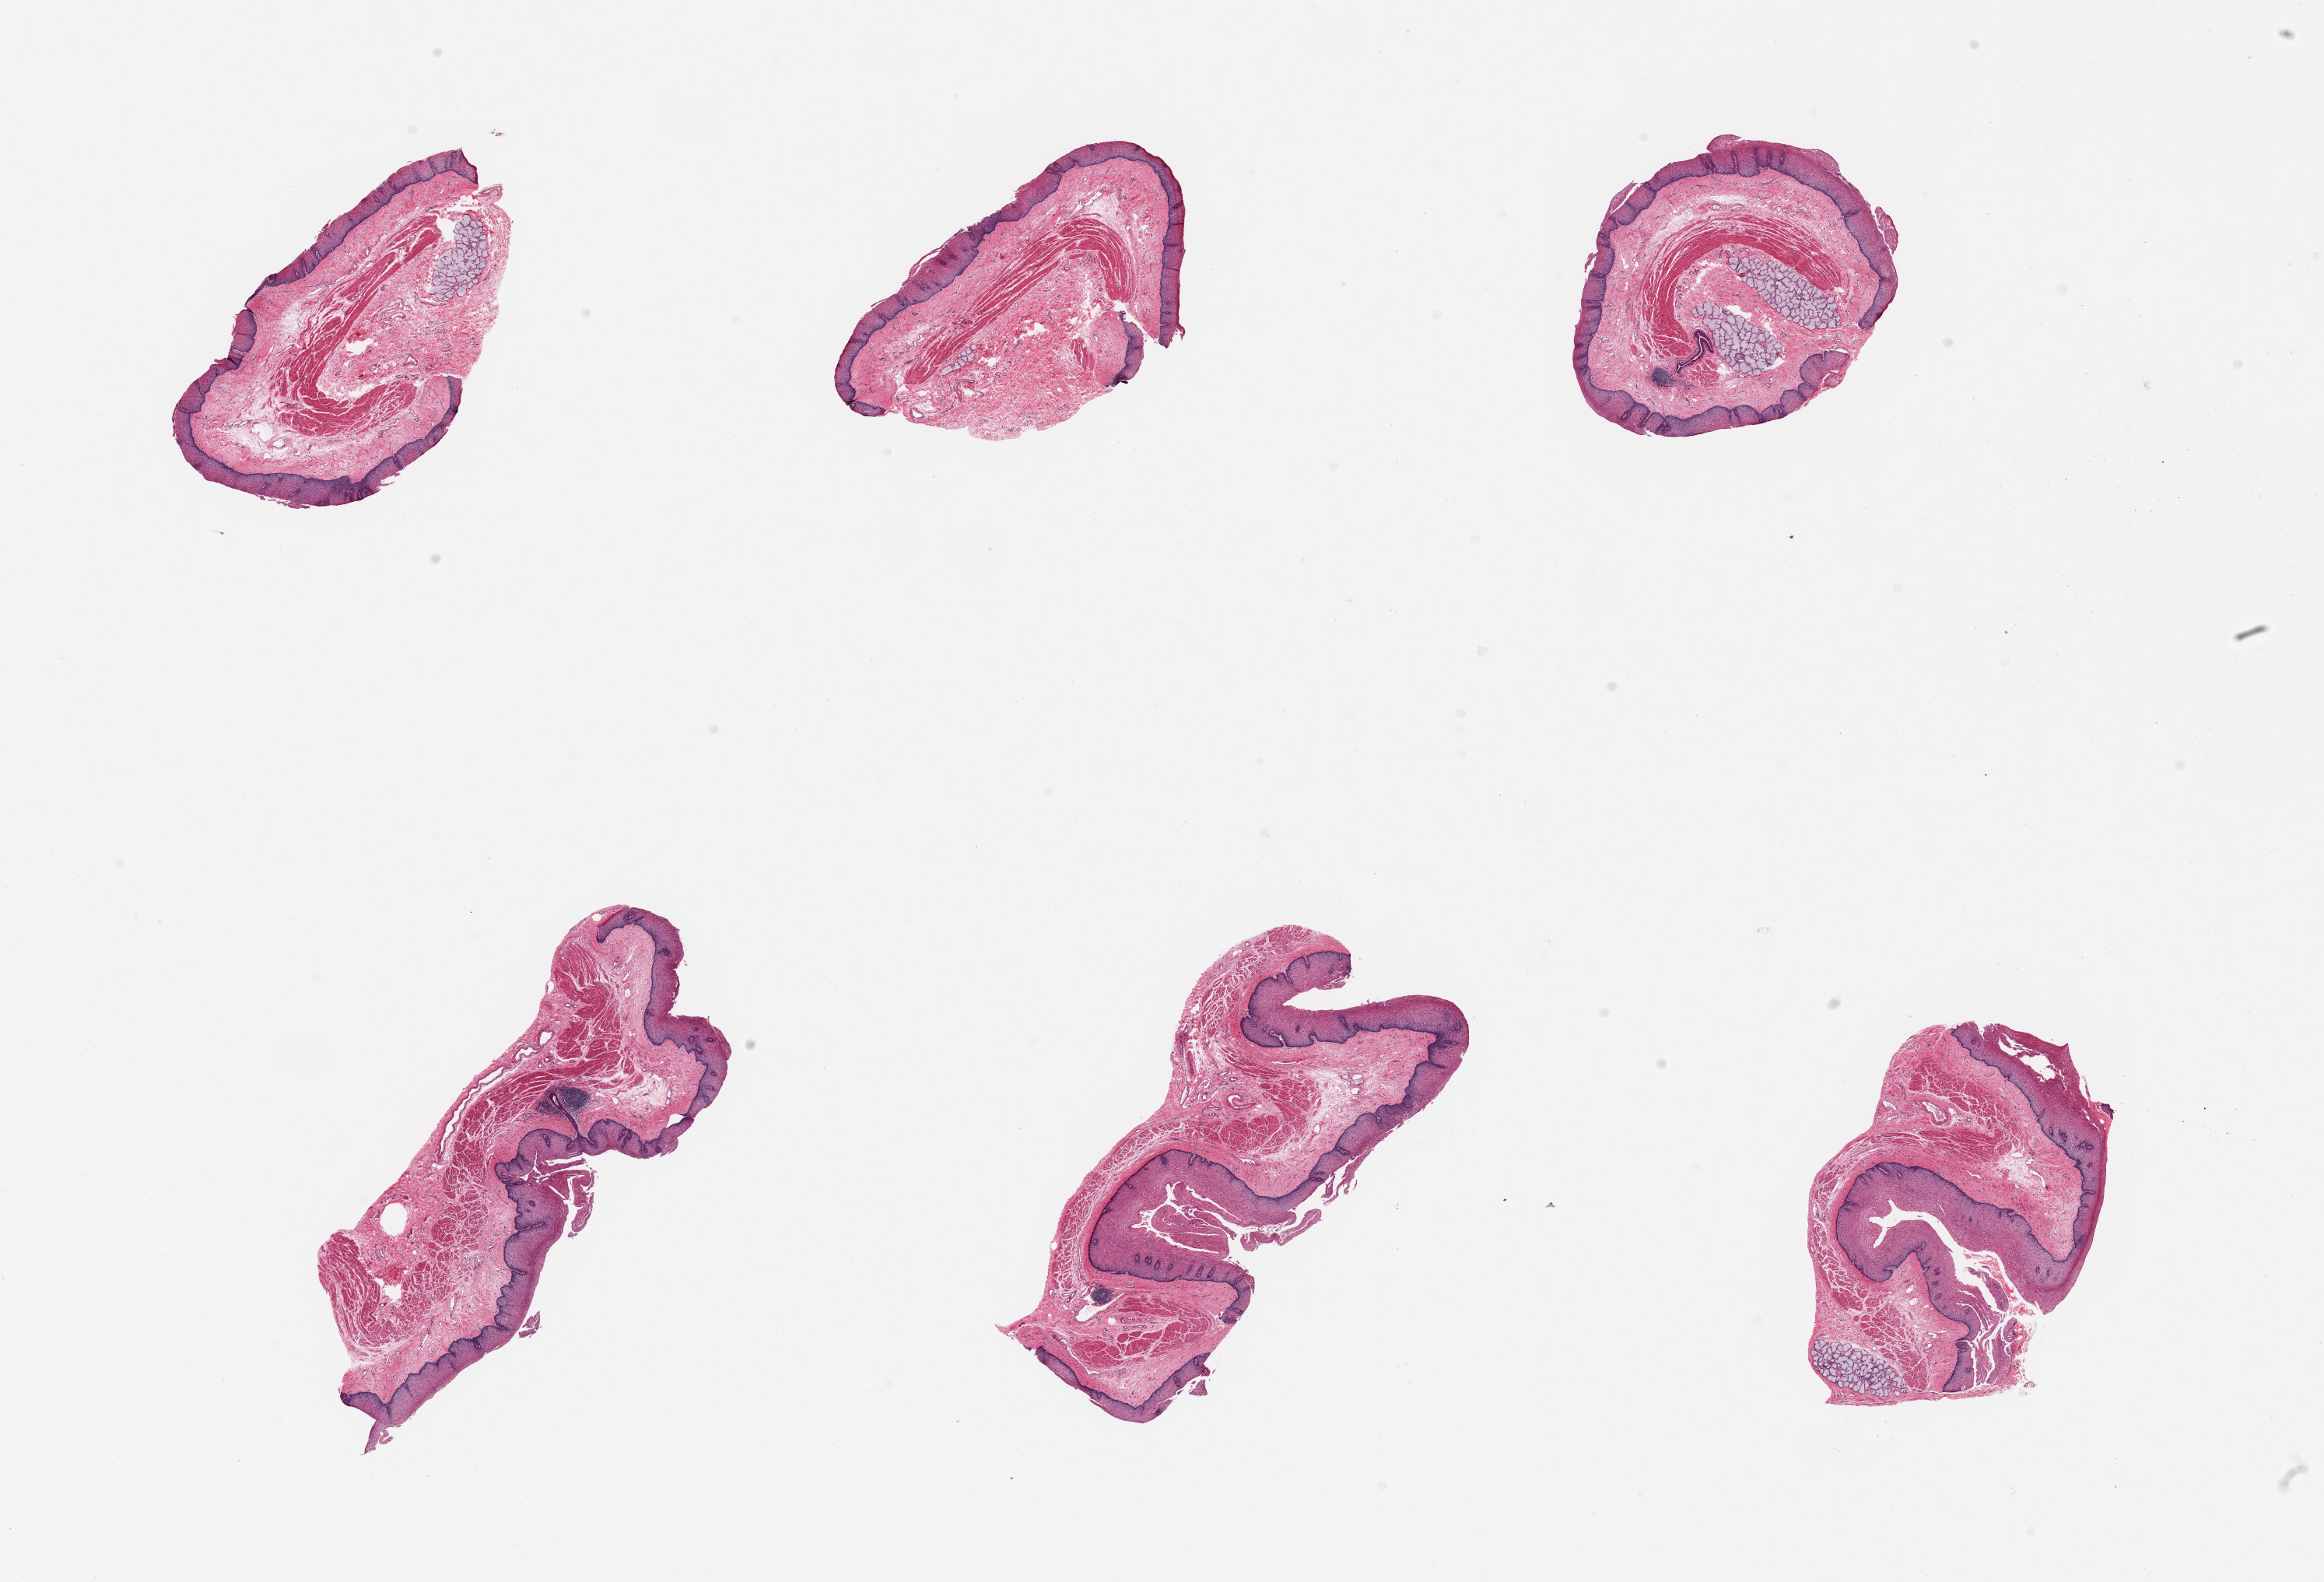
Digitized haematoxylin and eosin-stained section, brightfield — whole scanned area (about 23.6 x 16.1 mm, slide scanned at 20x) shown as a low-resolution overview, PAXgene-fixed paraffin-embedded (PFPE) section, section of esophageal mucous membrane (target tissue), donor tissue sample. Donor sex: male.
* reviewer comment on this tissue sample: 6 pieces, squamous mucosa is ~0.2-0.3mm, ~20-50% thickness; Submucosal mucus glands present